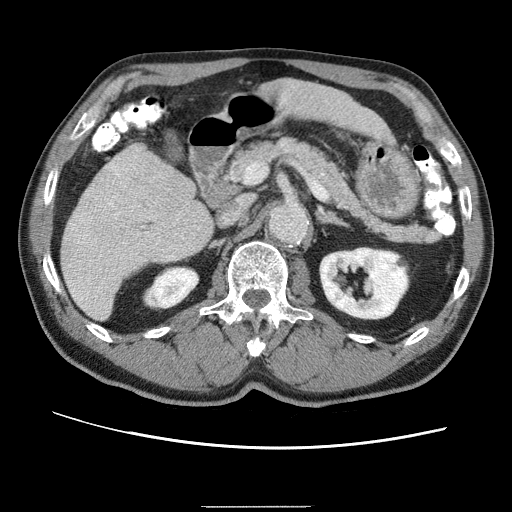
Contrast-enhanced abdominal CT (liver protocol), one axial slice. Position 21 of 75 along the scan axis. 120 kVp. One of 2 acquisitions stored at this slice position. Soft-tissue window (W 400 / L 40 HU). 512 × 512 image matrix. From the clinical record (not read from this slice): diagnosis: hepatocellular carcinoma (patient treated with transarterial chemoembolisation; whether this scan precedes or follows treatment is not stated here); TNM stage (as recorded): Stage-II; Child-Pugh class: A; tumour nodularity: multinodular.
Outlined on this slice (semi-automatic segmentation, software-assisted and operator-edited):
- liver parenchyma outside the tumour (the mass and vessels are separate outlines, so this box may not span the whole liver): bounding box (x1, y1, x2, y2) in pixels: (62, 146, 208, 318)
- liver vessels: (86, 158, 149, 257)